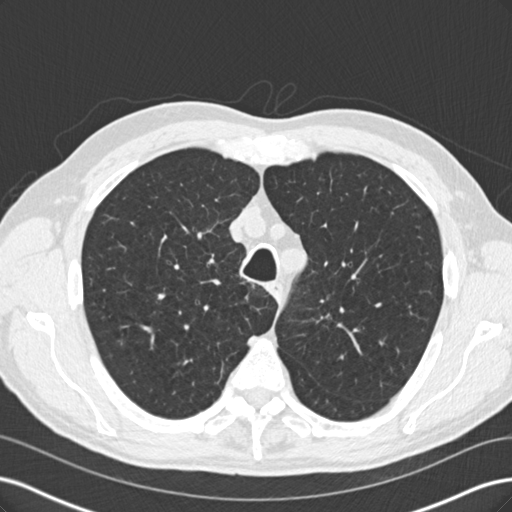
Low-dose screening chest CT, one axial slice; slice 173 of 219 in the series (ordered by position); 120 kVp; lung window (W 1500 / L -600 HU); 2 mm slice thickness; 512 × 512 image matrix, field of view 360 × 360 mm.
Structures marked on this image (outlined manually by an expert reader):
- lesion 1 (tumor, upper lobe of left lung): box from (x=322, y=313) to (x=330, y=319) px